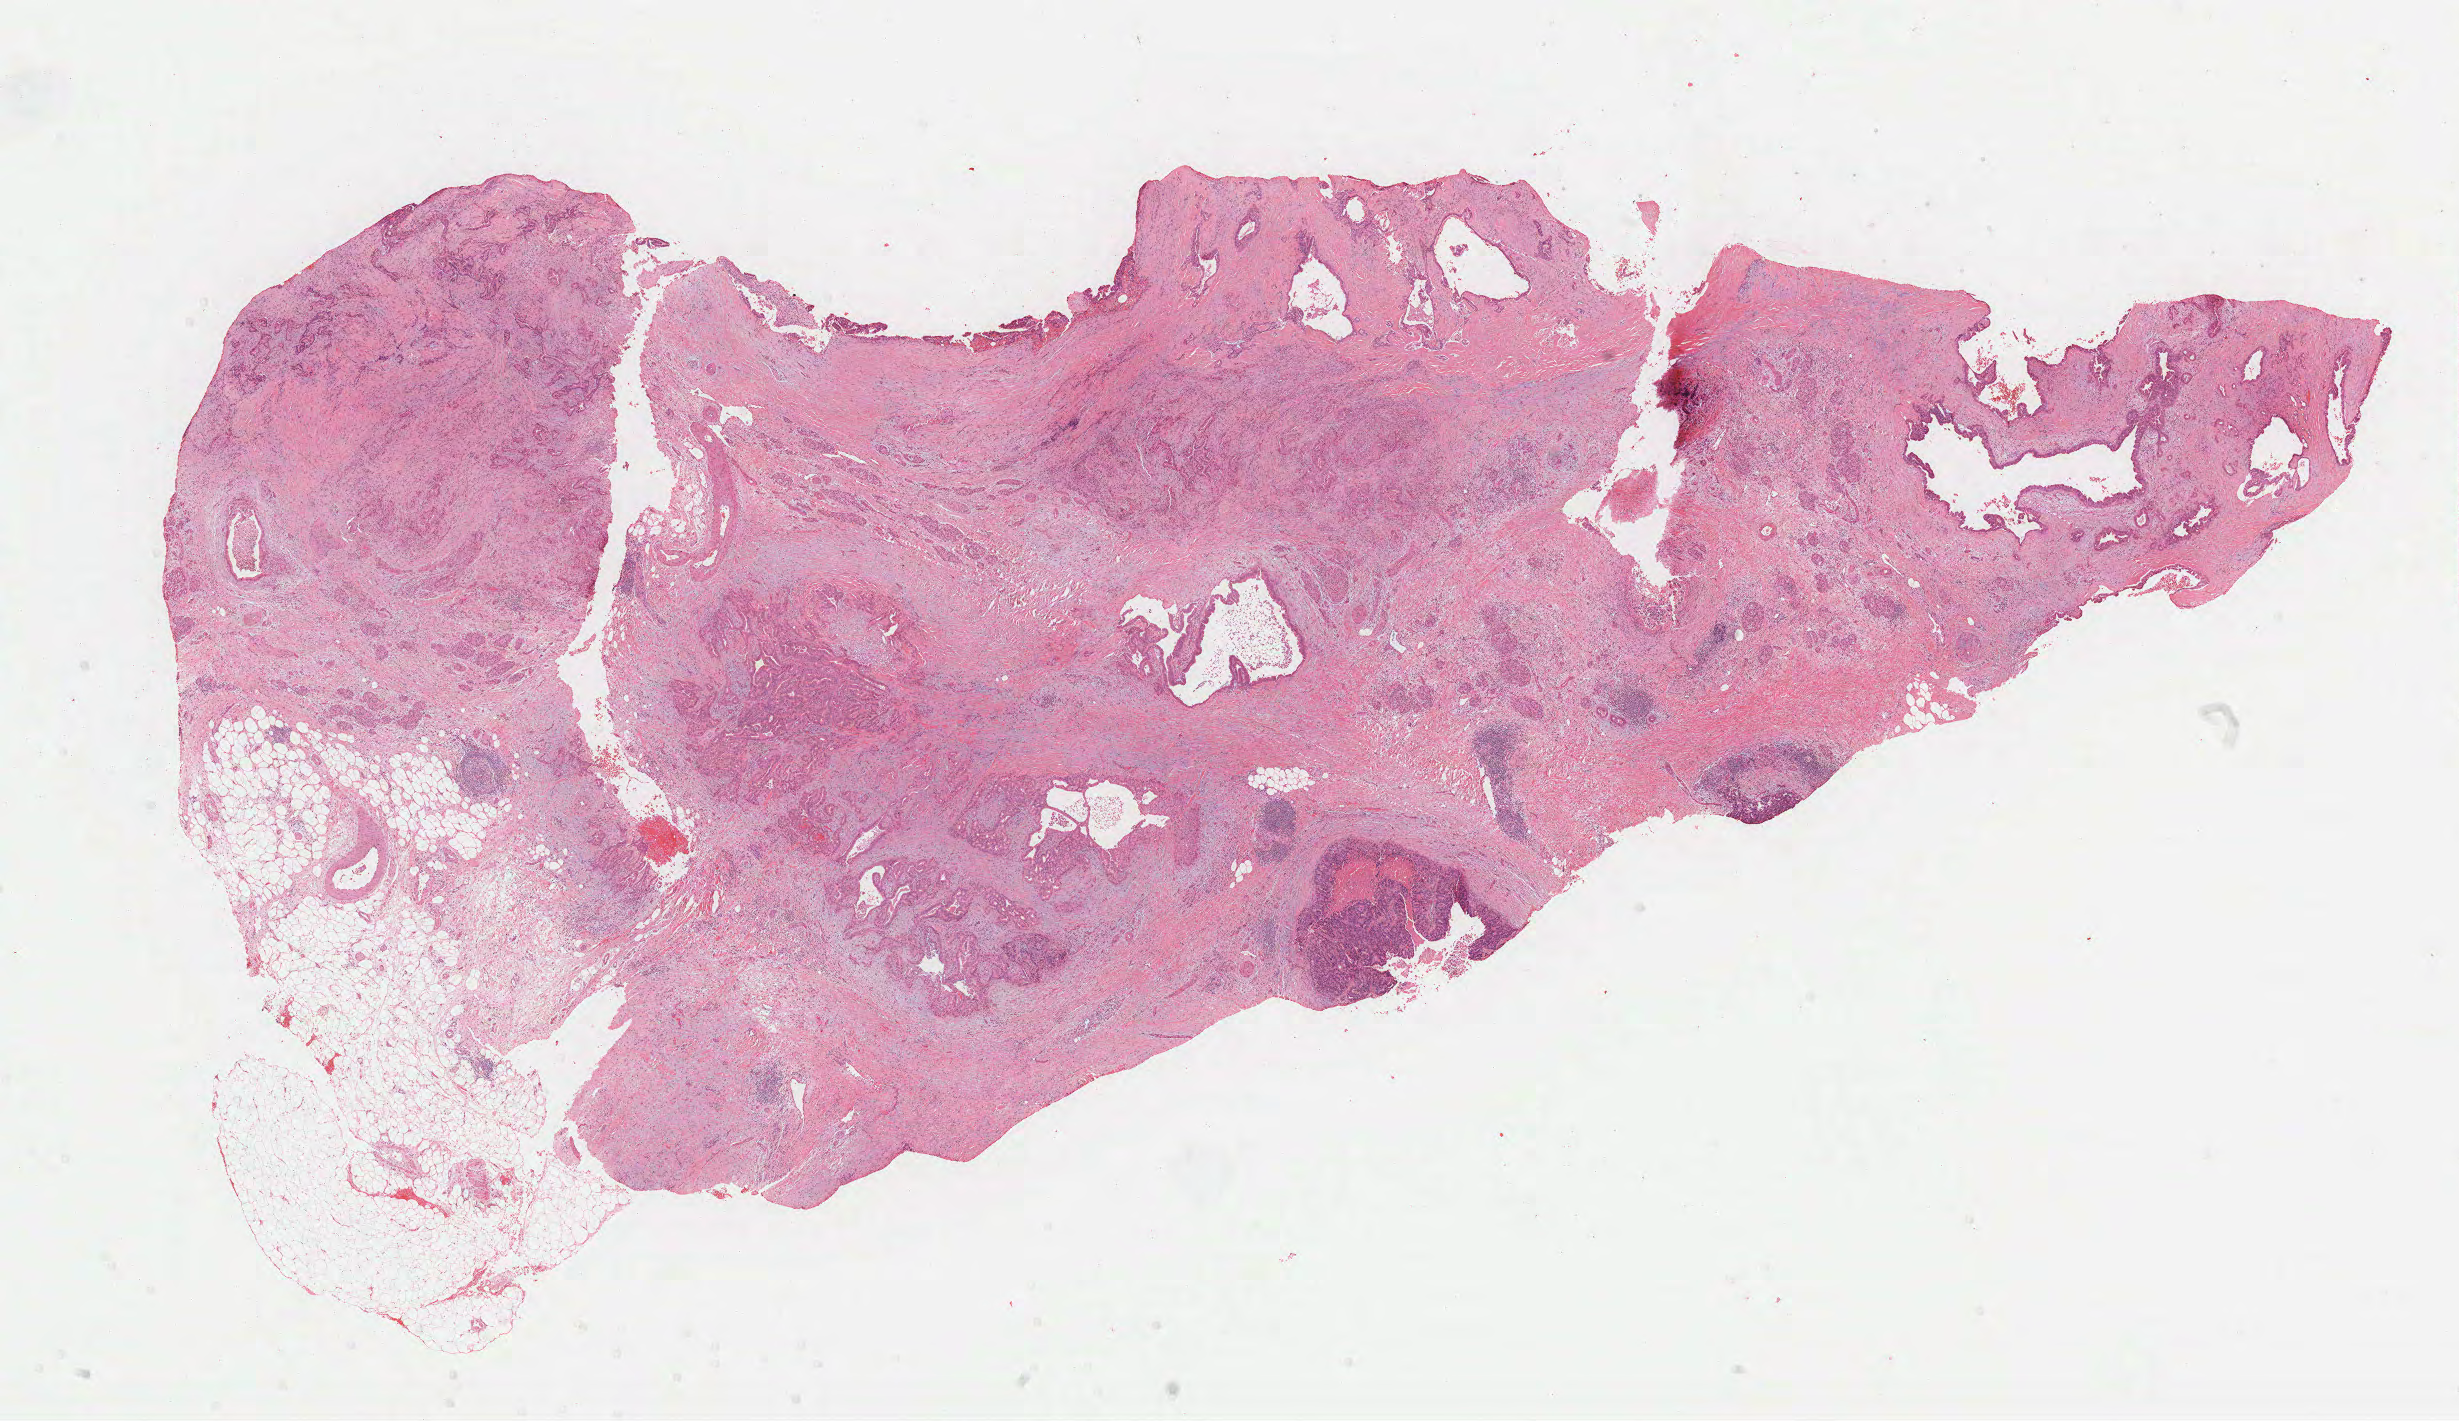
Whole-slide histology image, H&E-stained, low-resolution overview of the scanned area, about 19.9 x 11.5 mm (slide scanned at 40x); FFPE section; sample: primary tumour, pancreas. Male, age 57 years at initial diagnosis.
Diagnosis: Infiltrating duct carcinoma, NOS (head of pancreas).